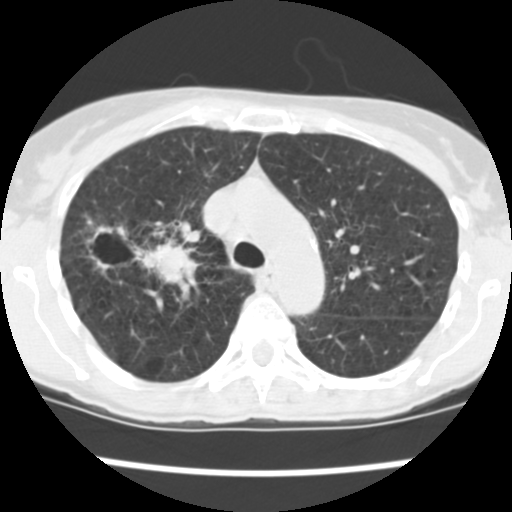
Chest CT (low-dose screening protocol), one axial image; baseline screening round; lung window (W 1500 / L -600 HU). Female participant, aged 60 years at enrolment. Current smoker at enrolment.
Lesion marked by an expert reader, bounding box (x1, y1, x2, y2) in pixels: (84, 216, 198, 285). The screening reader recorded 3 non-calcified nodules or masses ≥4 mm on this exam; which of them this box marks is not recorded.